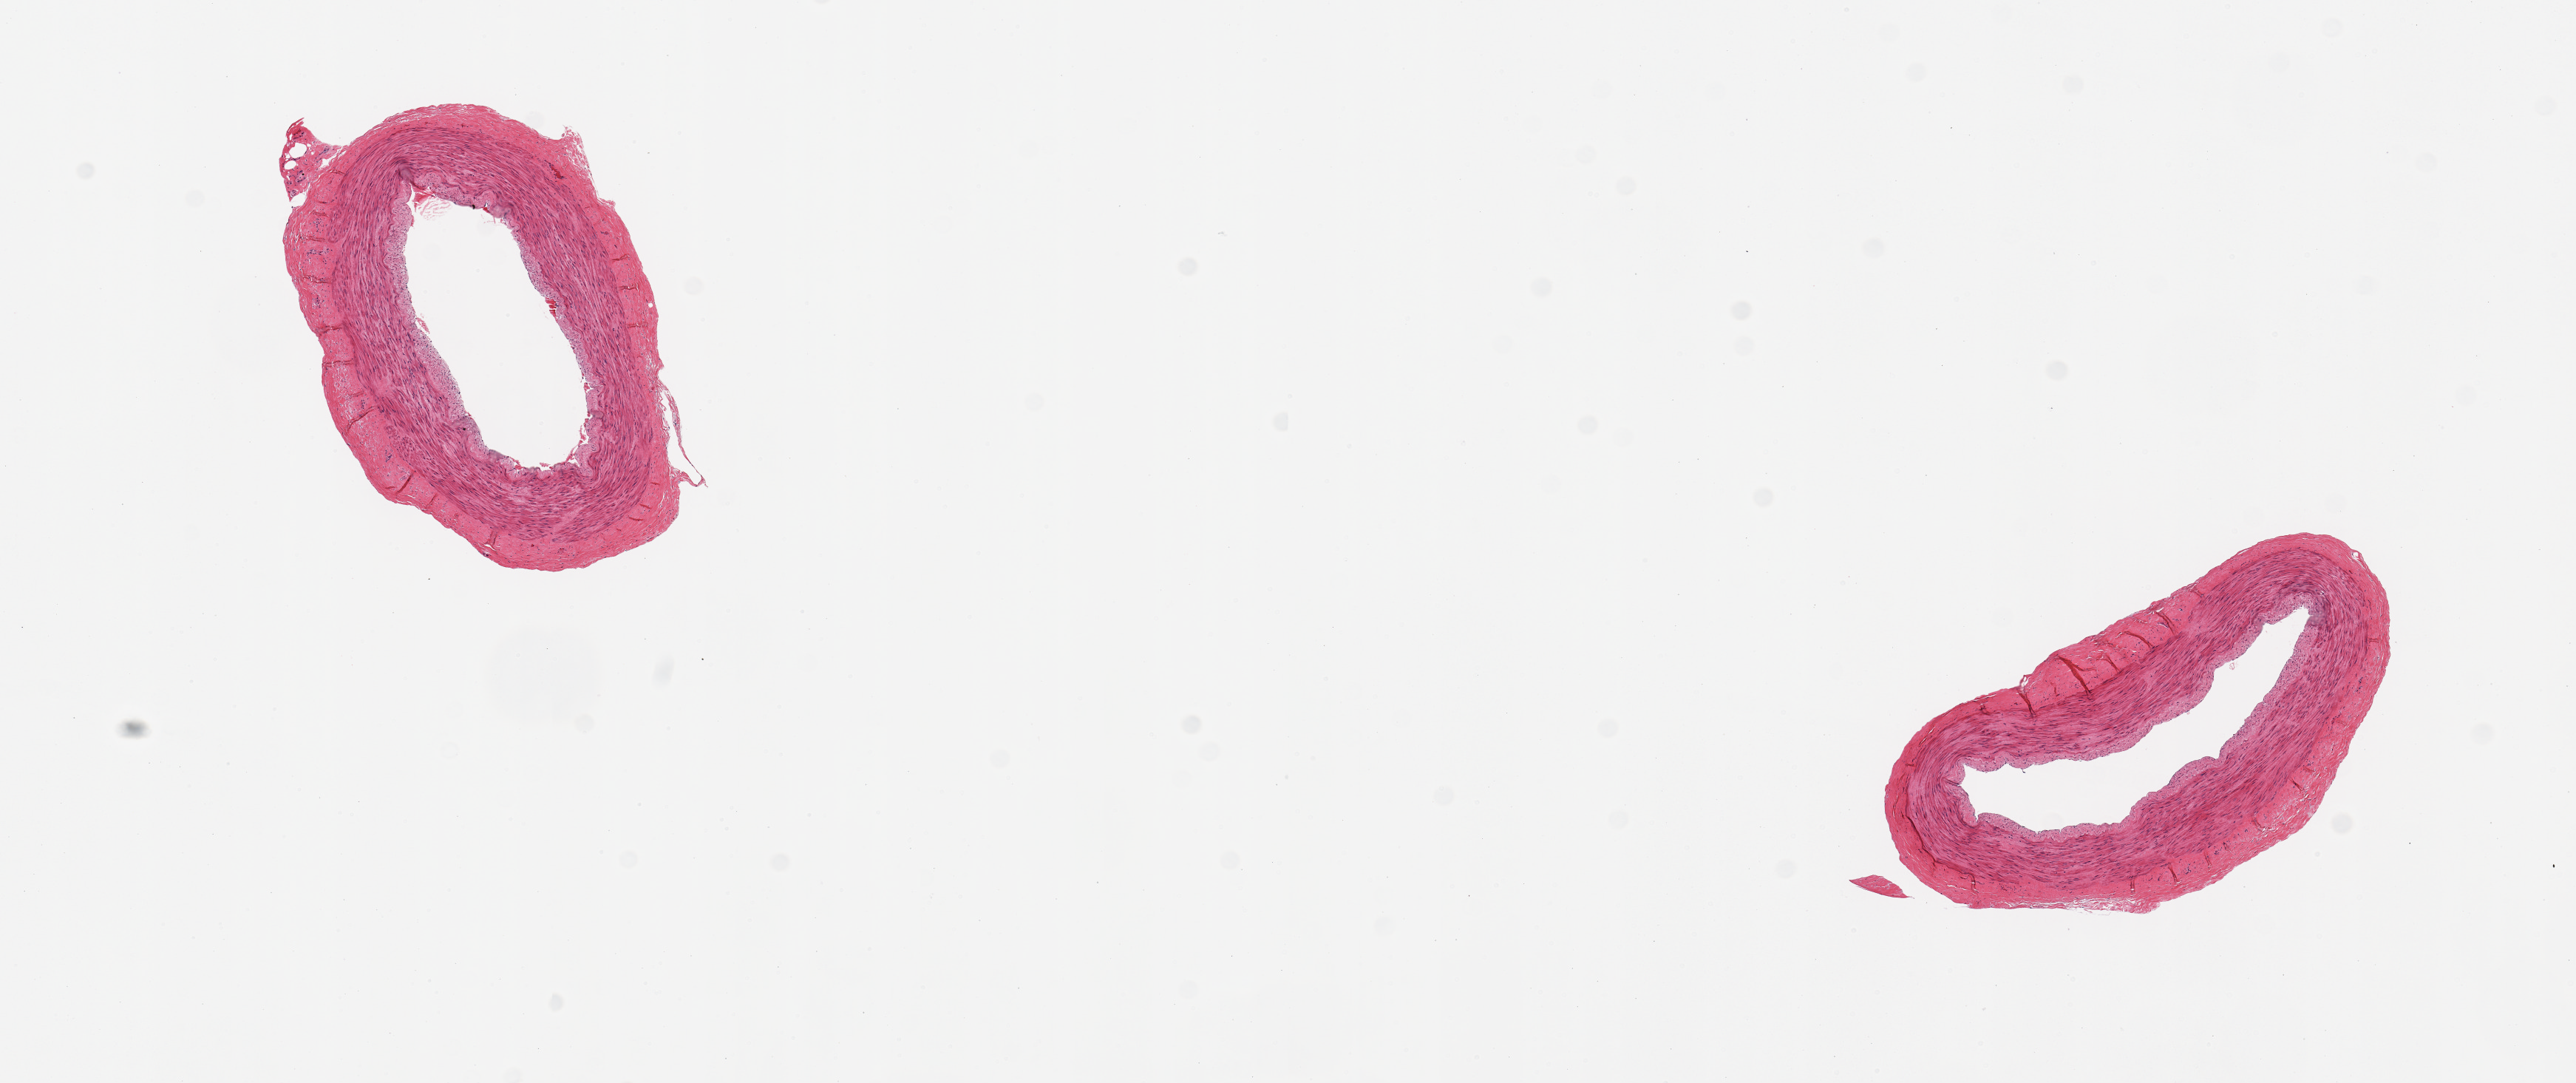
Digitized haematoxylin and eosin-stained section — whole scanned area (about 13.8 x 5.8 mm, acquisition: 20x scan) shown as a low-resolution overview. PAXgene-fixed paraffin-embedded (PFPE) section. Target tissue: tibial artery. Donor tissue sample. Donor sex: male.
• pathologist's review note for this sample: 2 pieces; well trimmed; no plaques